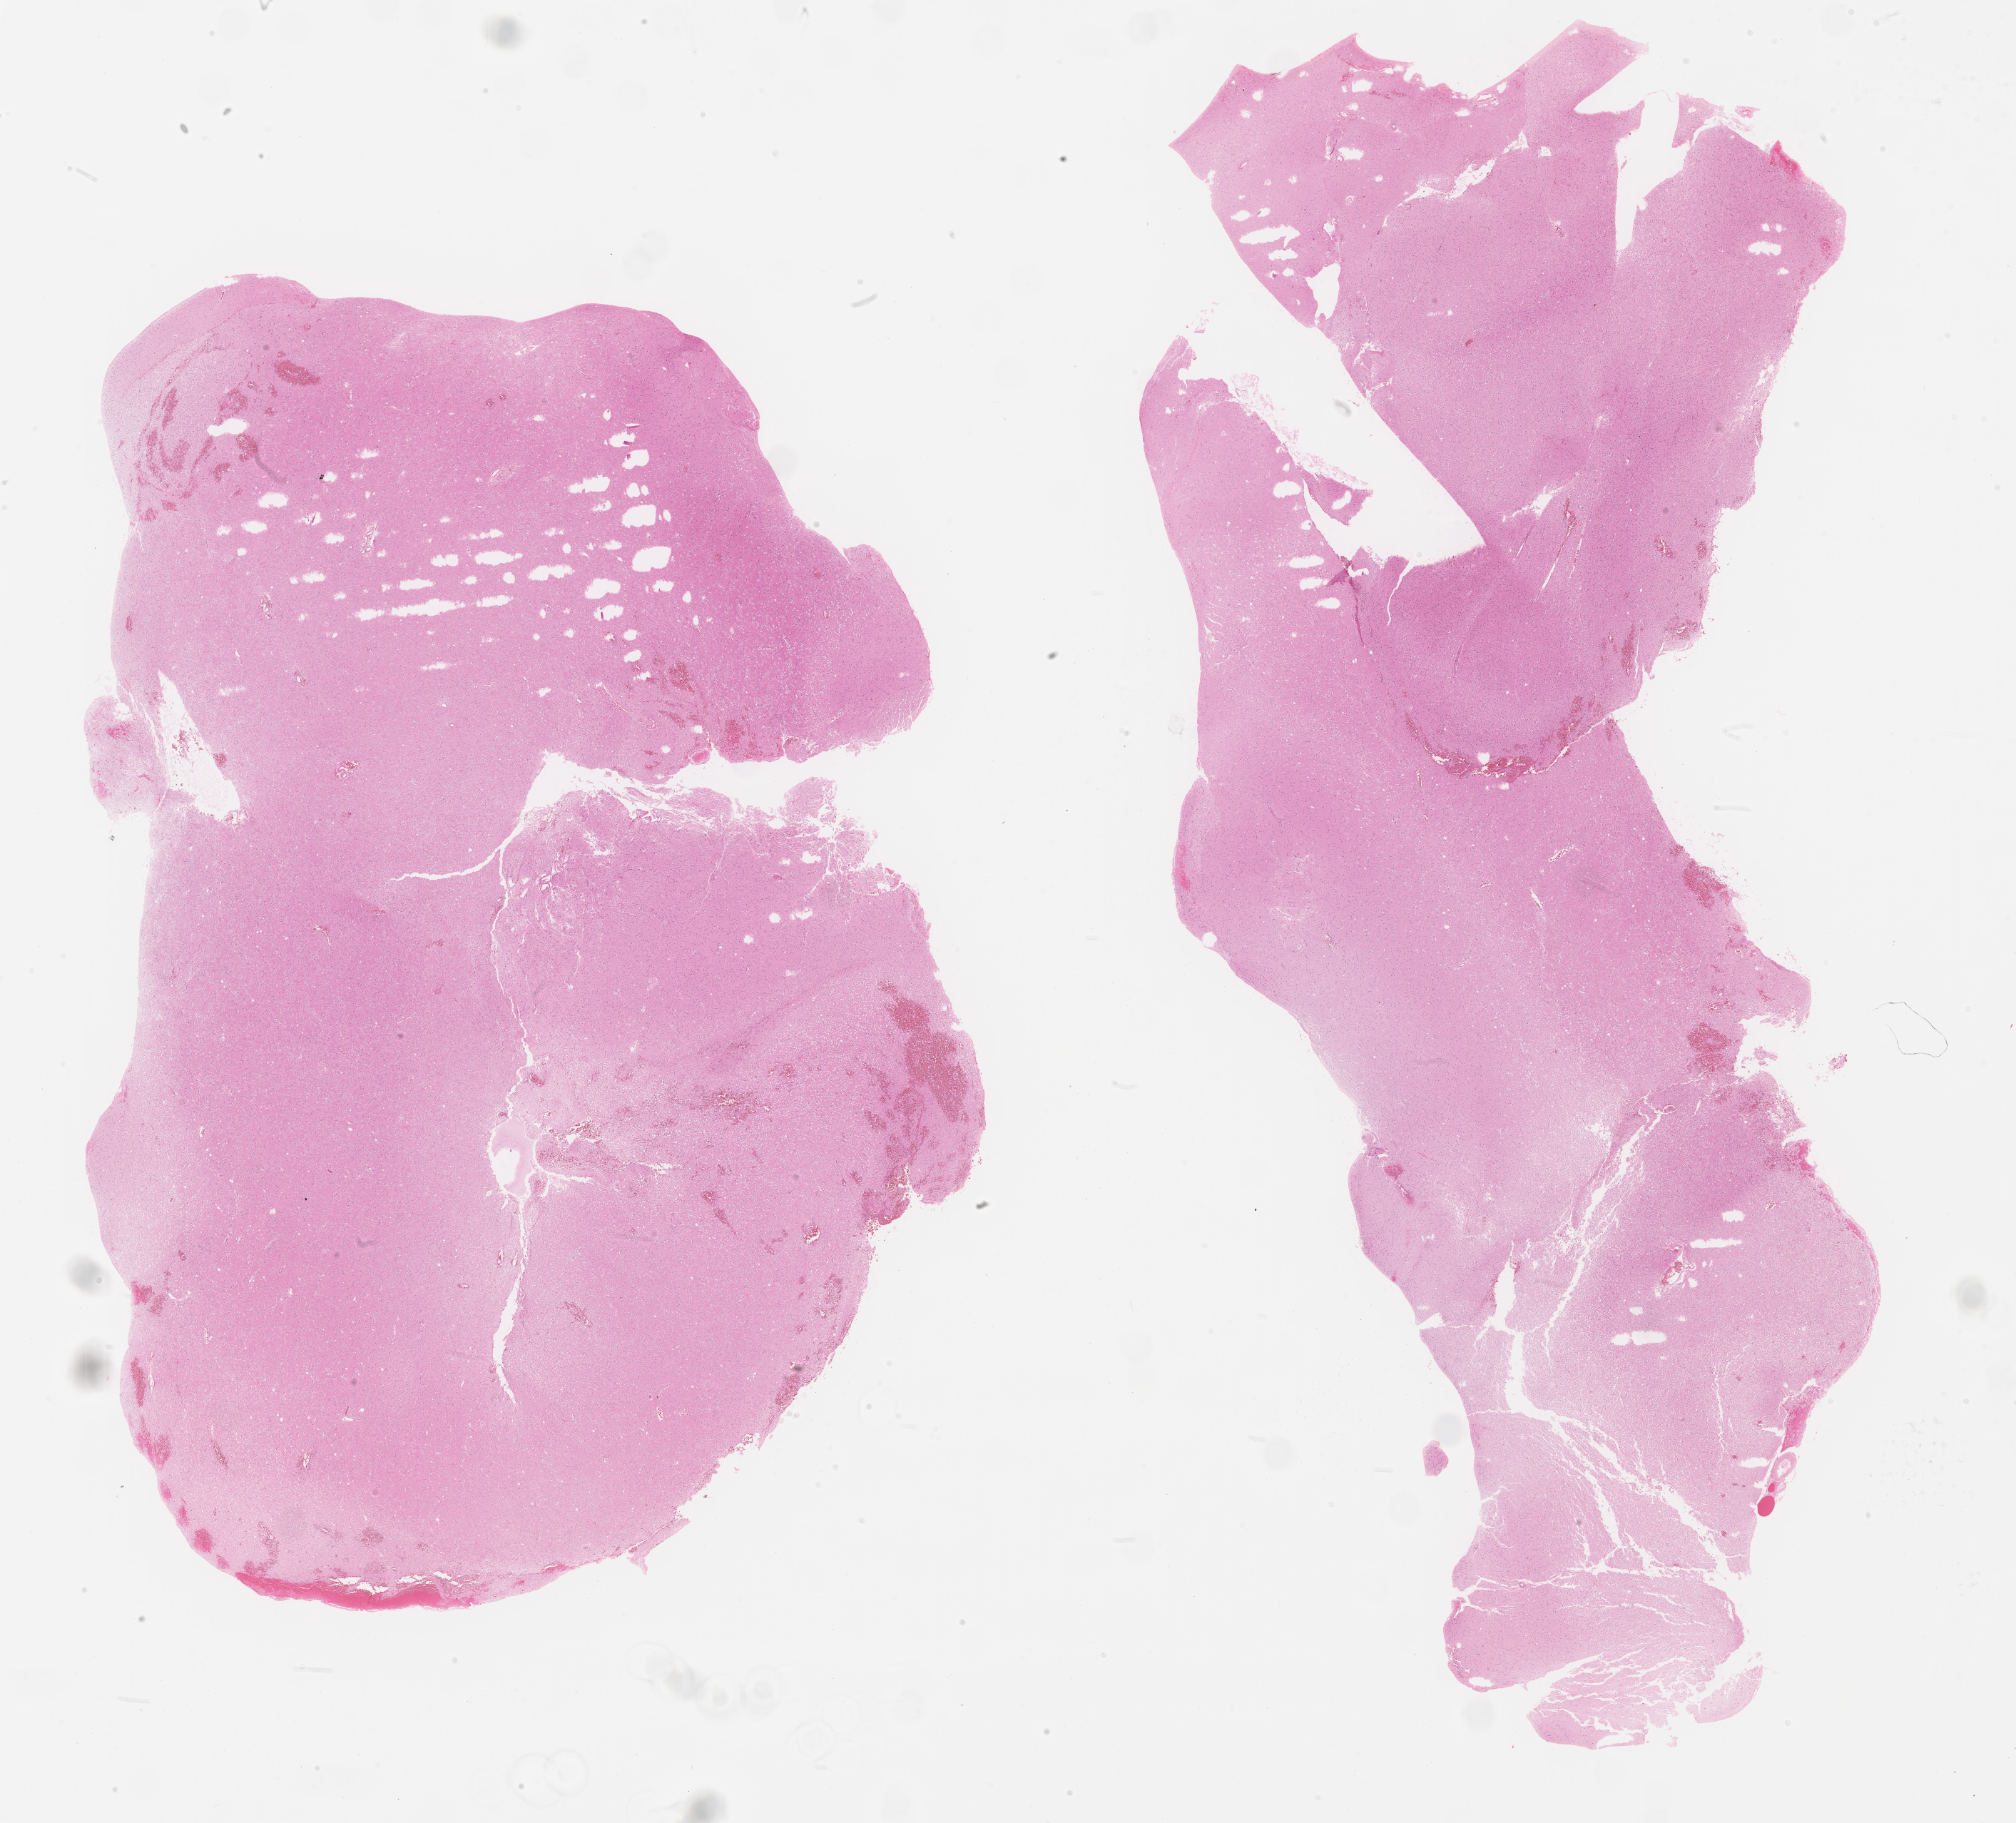
H&E whole-slide image, whole scanned area (about 22.8 x 20.6 mm, slide scanned at 40x) shown as a low-resolution overview. Formalin-fixed paraffin-embedded (FFPE) diagnostic section. Sample: primary tumour, brain. Male, age 40 years at initial diagnosis. Histologic grade: G2 (moderately differentiated).
Pathologic diagnosis: Oligodendroglioma, NOS (cerebrum). Laterality: right.